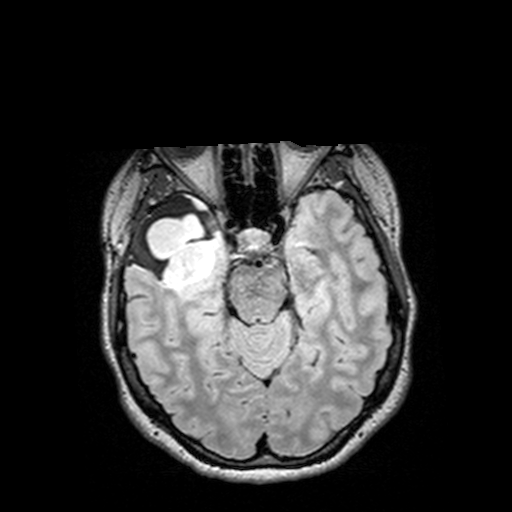
Brain MRI from a brain-tumour surgery series, one axial slice. Position 93 of 144 along the scan axis. T2 FLAIR. 1 mm slice thickness. 512 × 512 image matrix. From the clinical record (not read from this slice): histopathology: Astrocytoma; WHO grade: 3; IDH mutation: yes; tumour location: Right Insular Temporal.
Annotated regions visible in this slice (outlined manually by an expert reader):
- tumour: bounding box (x1, y1, x2, y2) in pixels: (126, 193, 232, 308)